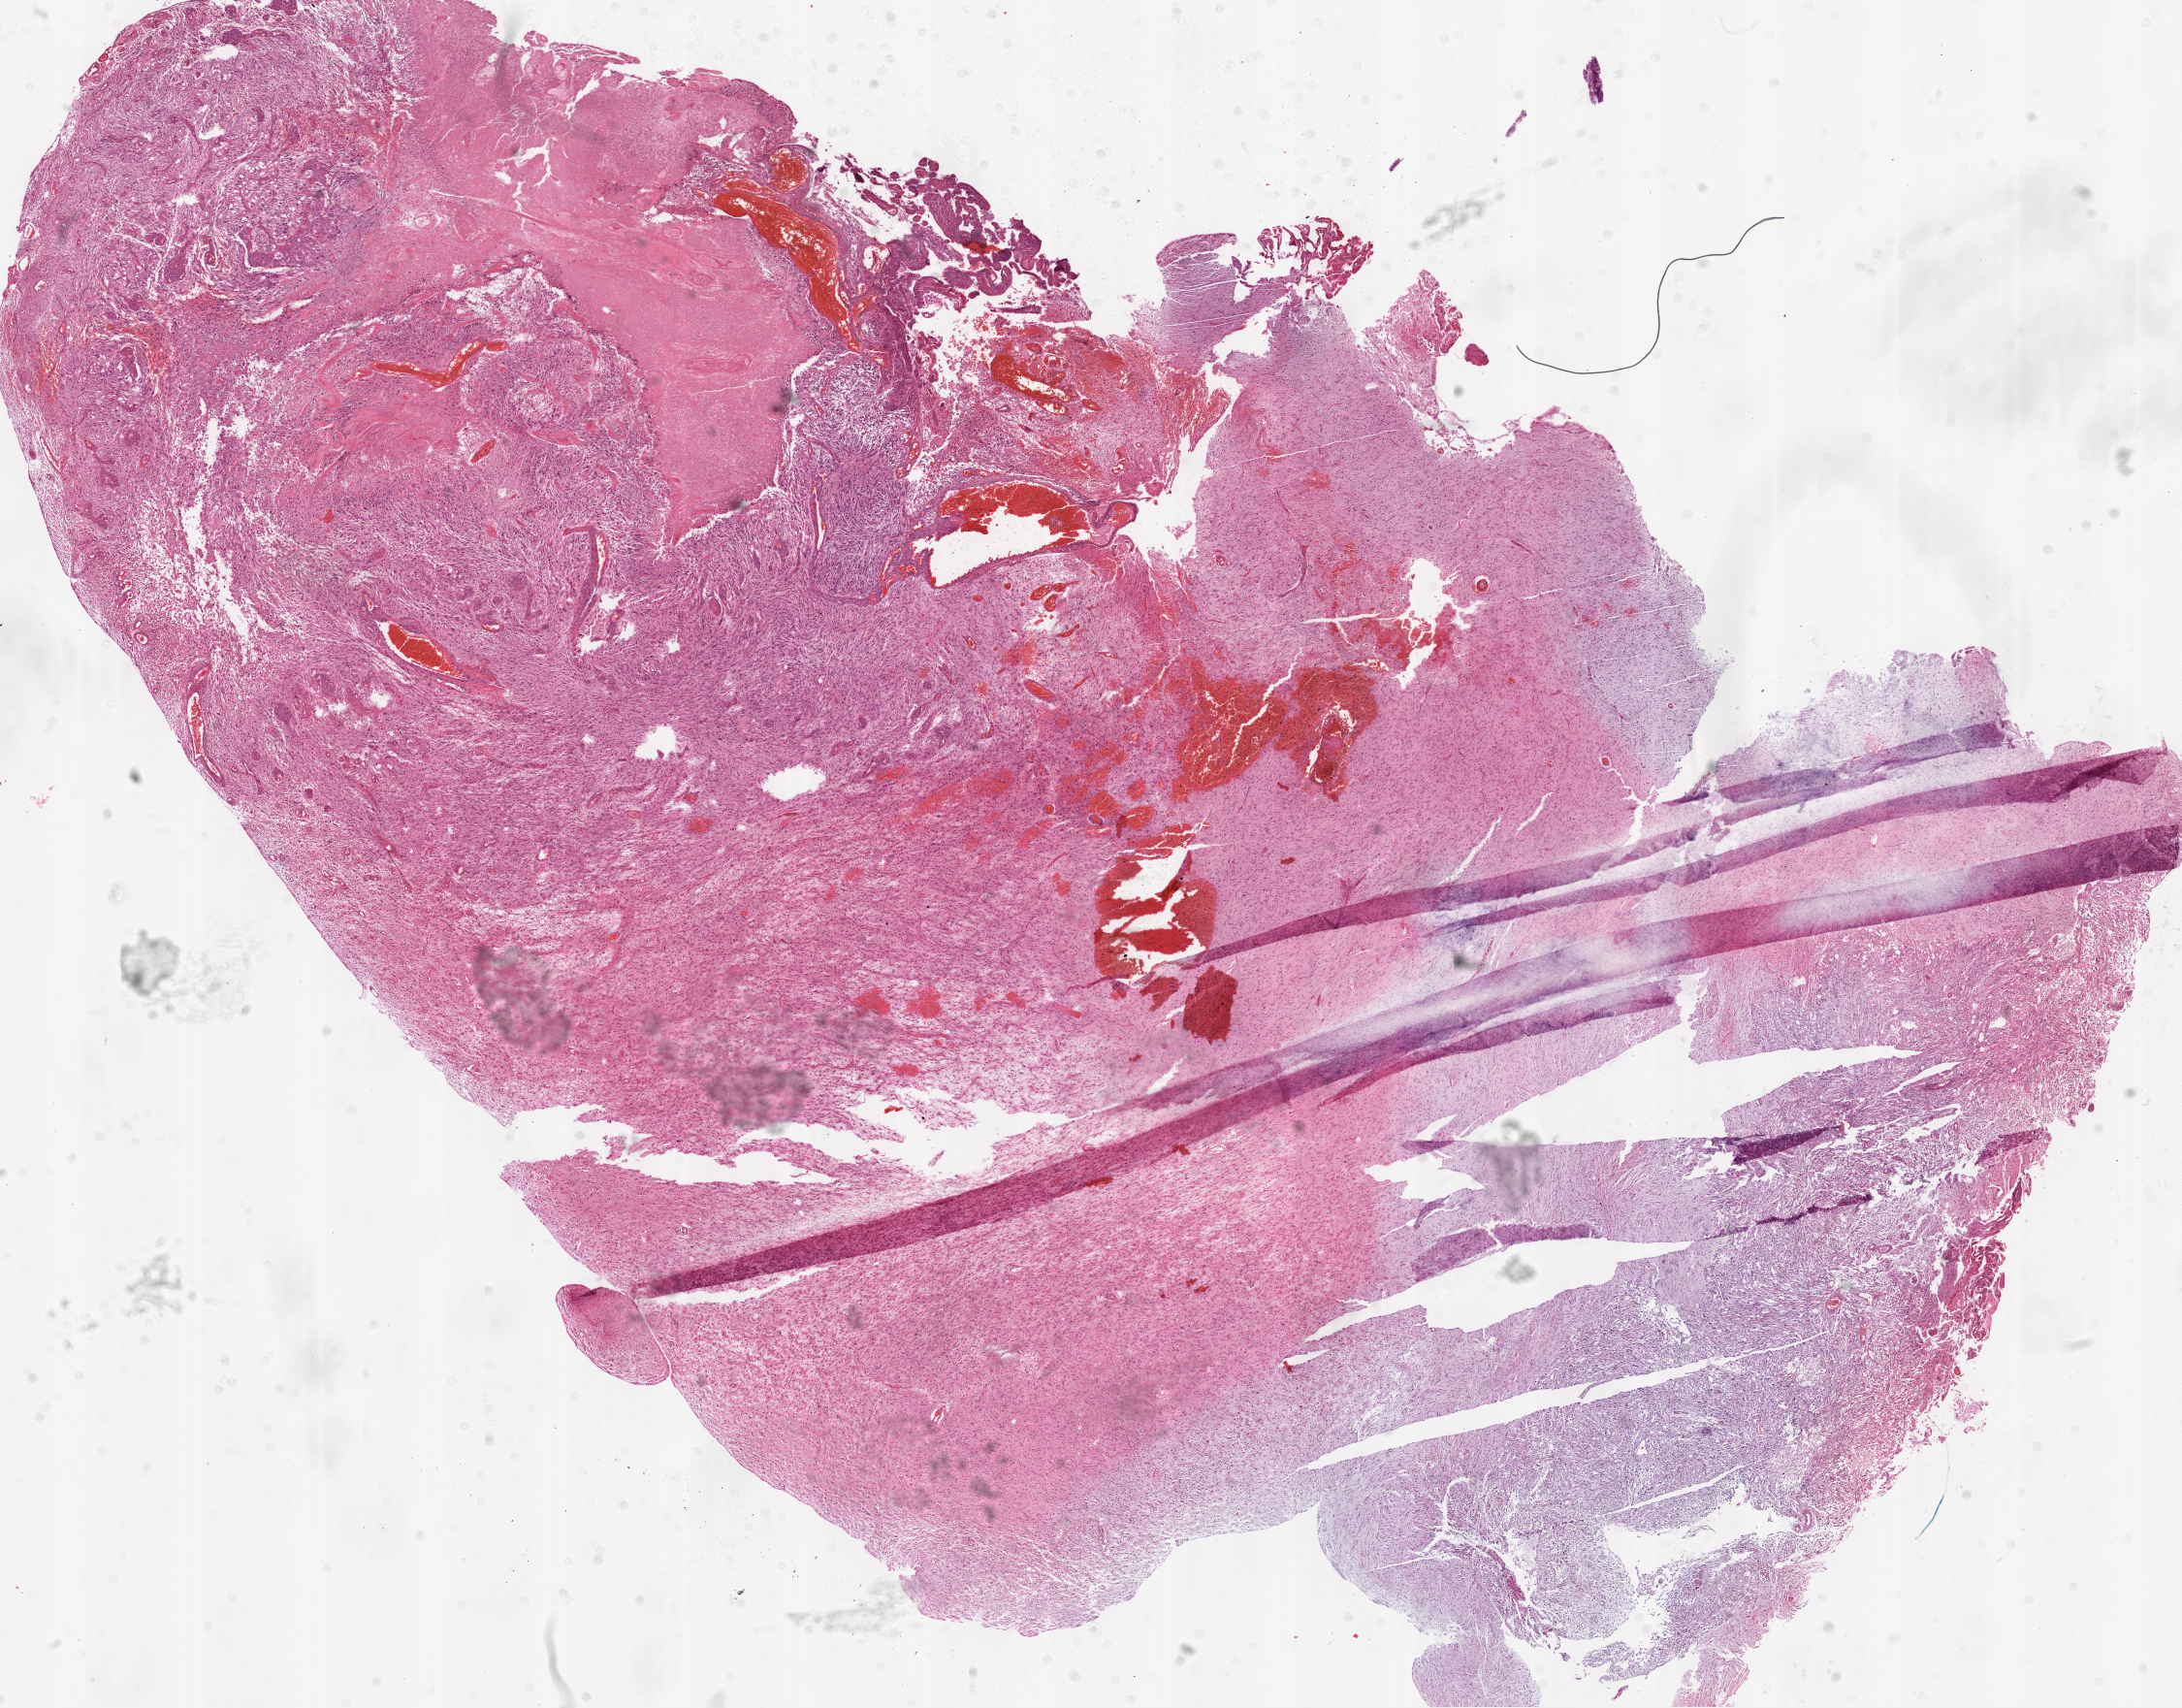
Whole-slide histology image, Hematoxylin and eosin (H&E) stained, a low-resolution overview of the entire scanned area, about 18.1 x 14.1 mm, FFPE section, primary tumour sample from the brain. Patient: female, age at initial diagnosis 62 years.
Diagnosis: Glioblastoma.